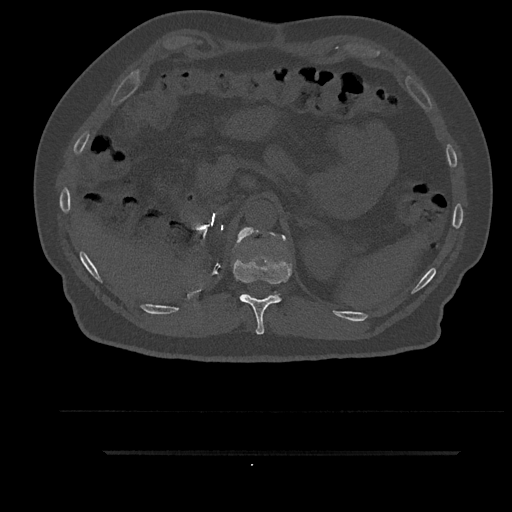
CT including the spine, one axial slice. Position 285 of 797 along the scan axis. Reconstruction kernel Br40s/3. Bone window (W 1800 / L 400 HU). 0.5 mm slice thickness. 512 × 512 image matrix. Patient: male, 63 years. Case-level facts recorded for this patient, not image findings: primary cancer: renal.
Structures marked on this image (semi-automatic segmentation, software-assisted and operator-edited):
- T11 vertebra: bounding box (x1, y1, x2, y2) in pixels: (232, 228, 292, 335)
- T12 vertebra: (236, 227, 286, 245)